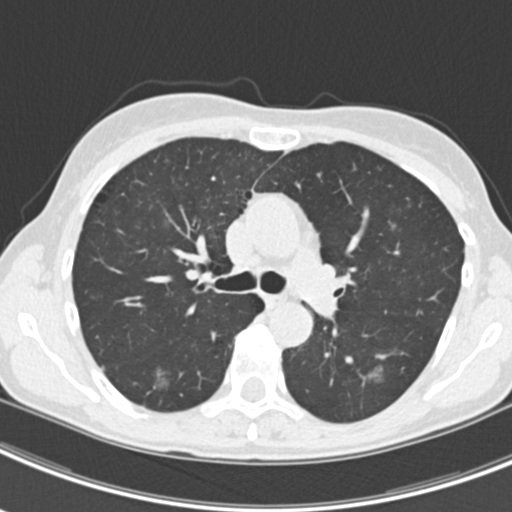
Axial slice from a low-dose chest CT screening exam. Second screening round (one year after baseline). Lung window (W 1500 / L -600 HU). Slice 71 of 219 in the series. 512 × 512 image matrix. Female participant, aged 63 years at enrolment. Current smoker at enrolment.
- 2 expert-annotated lung lesions on this slice (largest first), box from (x=365, y=359) to (x=403, y=393) px; (x=144, y=363)–(x=177, y=396).
- The screening reader recorded 9 non-calcified nodules or masses ≥4 mm on this exam; which of them these boxes mark is not recorded.
- Official screen result: positive, other.
- Lung cancer was diagnosed 408 days after this screen (after the third annual screen): bronchiolo-alveolar adenocarcinoma, NOS, right upper lobe, right middle lobe, right lower lobe, left upper lobe, left lower lobe, moderately differentiated (G2), stage IV (AJCC 6th edition).